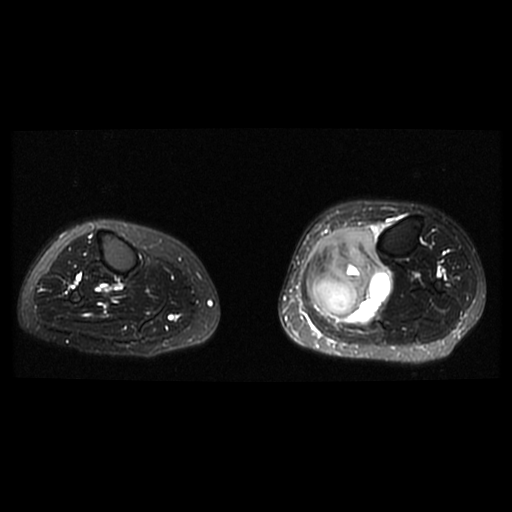
MRI of an extremity soft-tissue mass, one axial slice; position 16 of 38 along the scan axis; T2-weighted fat-saturated; 512 × 512 image matrix. Female patient. From the clinical record (not read from this slice): histological type: extraskeletal high grade osteogenic sarcoma; grade: high; site of the primary tumour: left calf.
Structures marked on this image (manually delineated by an expert):
- gross tumour volume (mass): bounding box <308,228,392,325> (left, top, right, bottom; pixels)